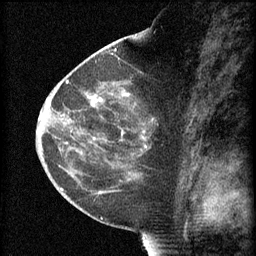
Breast MRI (dynamic contrast-enhanced), one sagittal slice. Position 34 of 60 along the scan axis. 3 images stored at this slice position (order not interpretable as contrast timing). 1.5 T. TE 4.2 ms, TR 8.2 ms. 256 × 256 image matrix, field of view 180 × 180 mm. Patient: female, 44 years.
Annotated regions visible in this slice (semi-automatically segmented with operator editing):
- analysis volume of interest (the breast-tissue region the enhancement analysis was run in; not a lesion): box from (x=73, y=82) to (x=161, y=165) px
- tumour enhancement mask (voxels above the 70 % enhancement threshold inside the analysis volume of interest): (x=91, y=94)–(x=146, y=141)